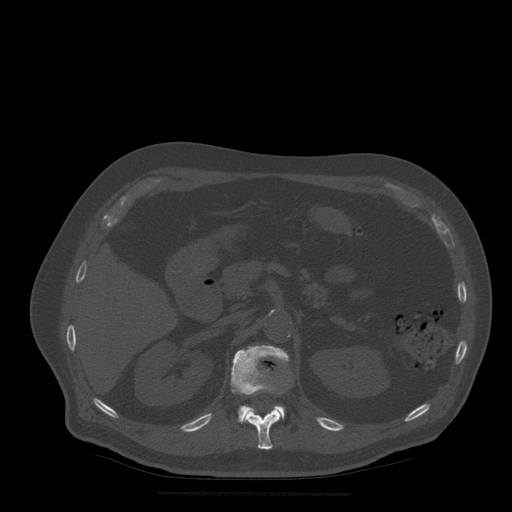
CT including the spine, one axial slice. Slice 209 of 522 in the series (ordered by position). Bone window (W 1800 / L 400 HU). 512 × 512 image matrix, field of view 420 × 420 mm. Patient age 72 years. Case-level facts recorded for this patient, not image findings: primary cancer: prostate.
Outlined on this slice (semi-automatically segmented with operator editing):
- L1 vertebra: bounding box (x1, y1, x2, y2) in pixels: (232, 345, 289, 423)
- T12 vertebra: (244, 391, 284, 450)